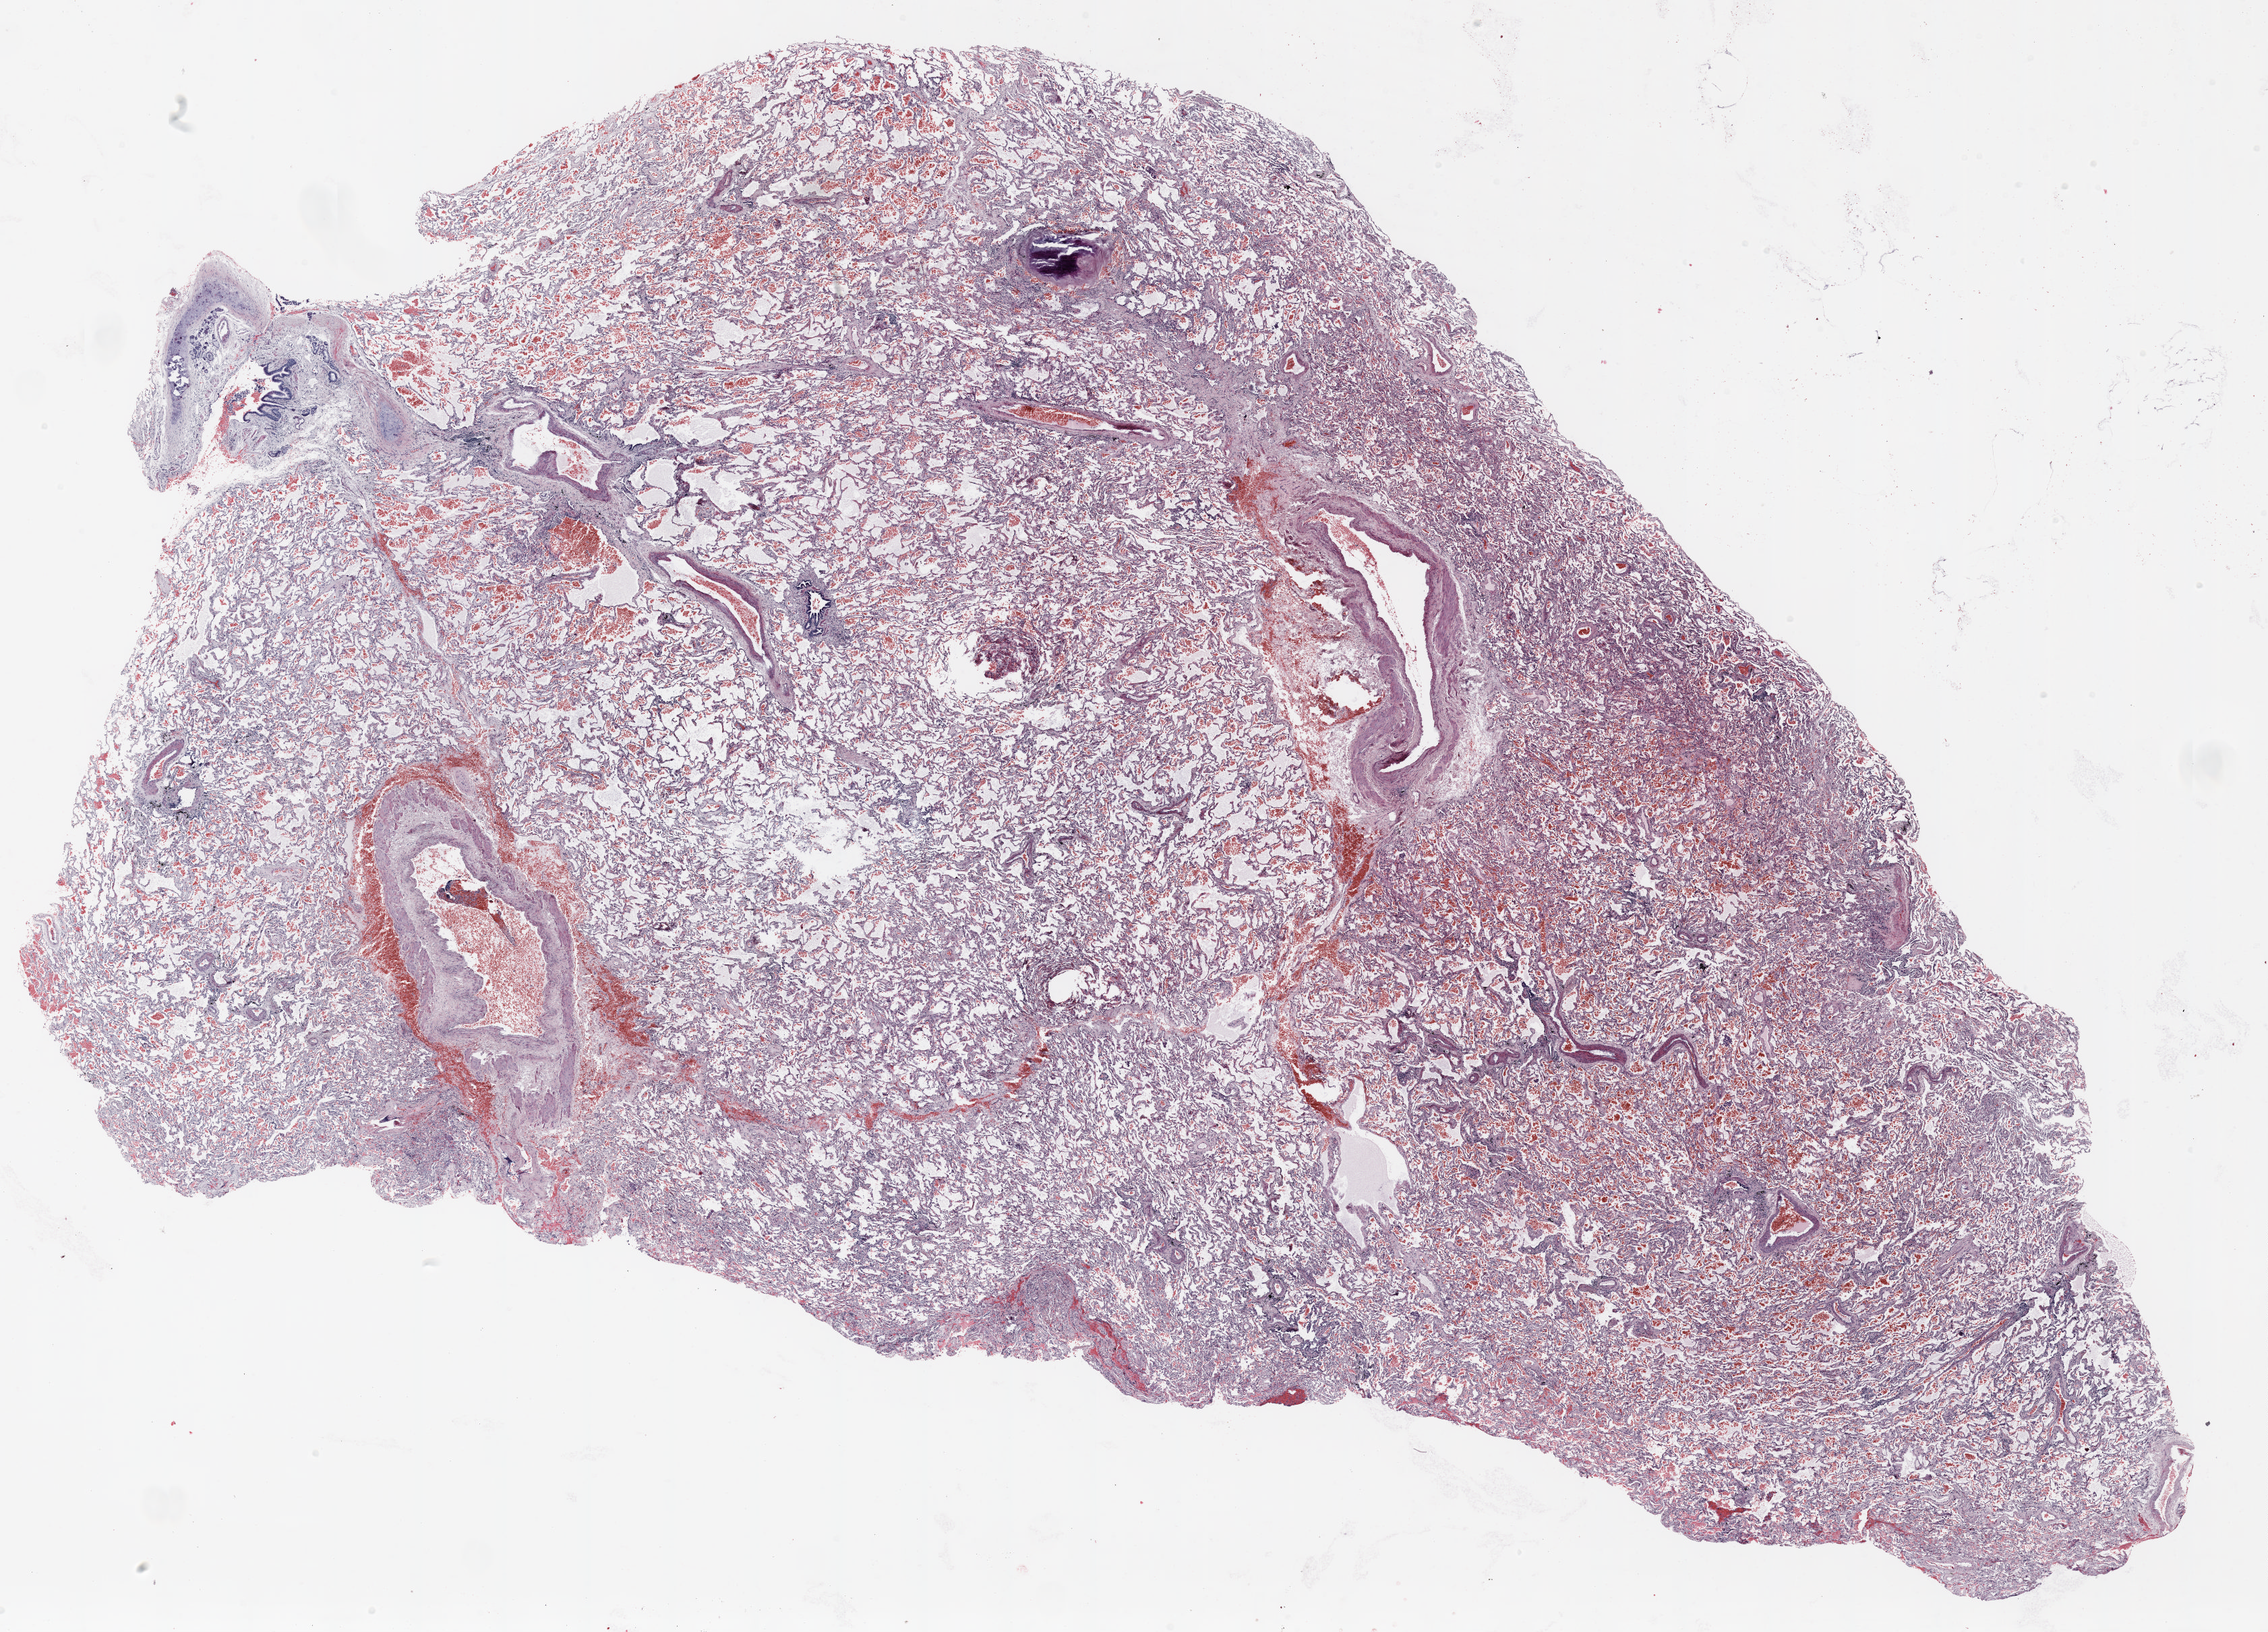
H&E-stained whole-slide image — whole scanned area (about 27.0 x 19.4 mm) shown as a low-resolution overview, FFPE section, lung. Female patient, aged 67 at enrolment. Former smoker at enrolment. Grade: poorly differentiated (G3).
Stage (AJCC 6th edition): IA. Primary tumour location (clinical record): right upper lobe. Participant's lung-cancer diagnosis: Adenocarcinoma with mixed subtypes. Tumour size (pathology): 30 mm.